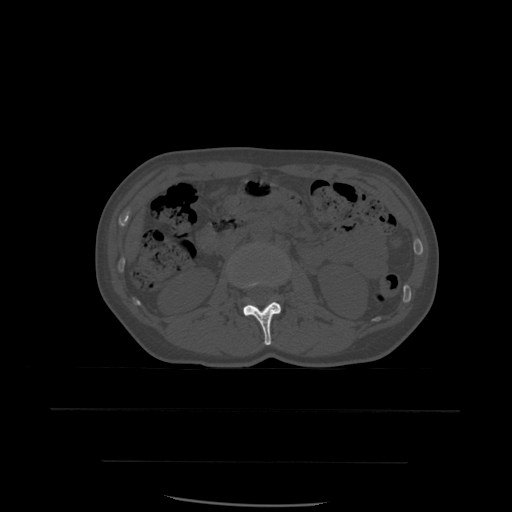
CT including the spine, one axial slice; slice 216 of 574 in the series (ordered by position); bone window (W 1800 / L 400 HU); 1.25 mm slice thickness; 512 × 512 image matrix, field of view 392 × 392 mm. Patient age 48 years. From the clinical record (not read from this slice): primary cancer: lung; vertebrae with lytic lesions (as recorded): T11.
Outlined on this slice (semi-automatic segmentation, software-assisted and operator-edited):
- L2 vertebra: bounding box <231,279,282,346> (left, top, right, bottom; pixels)